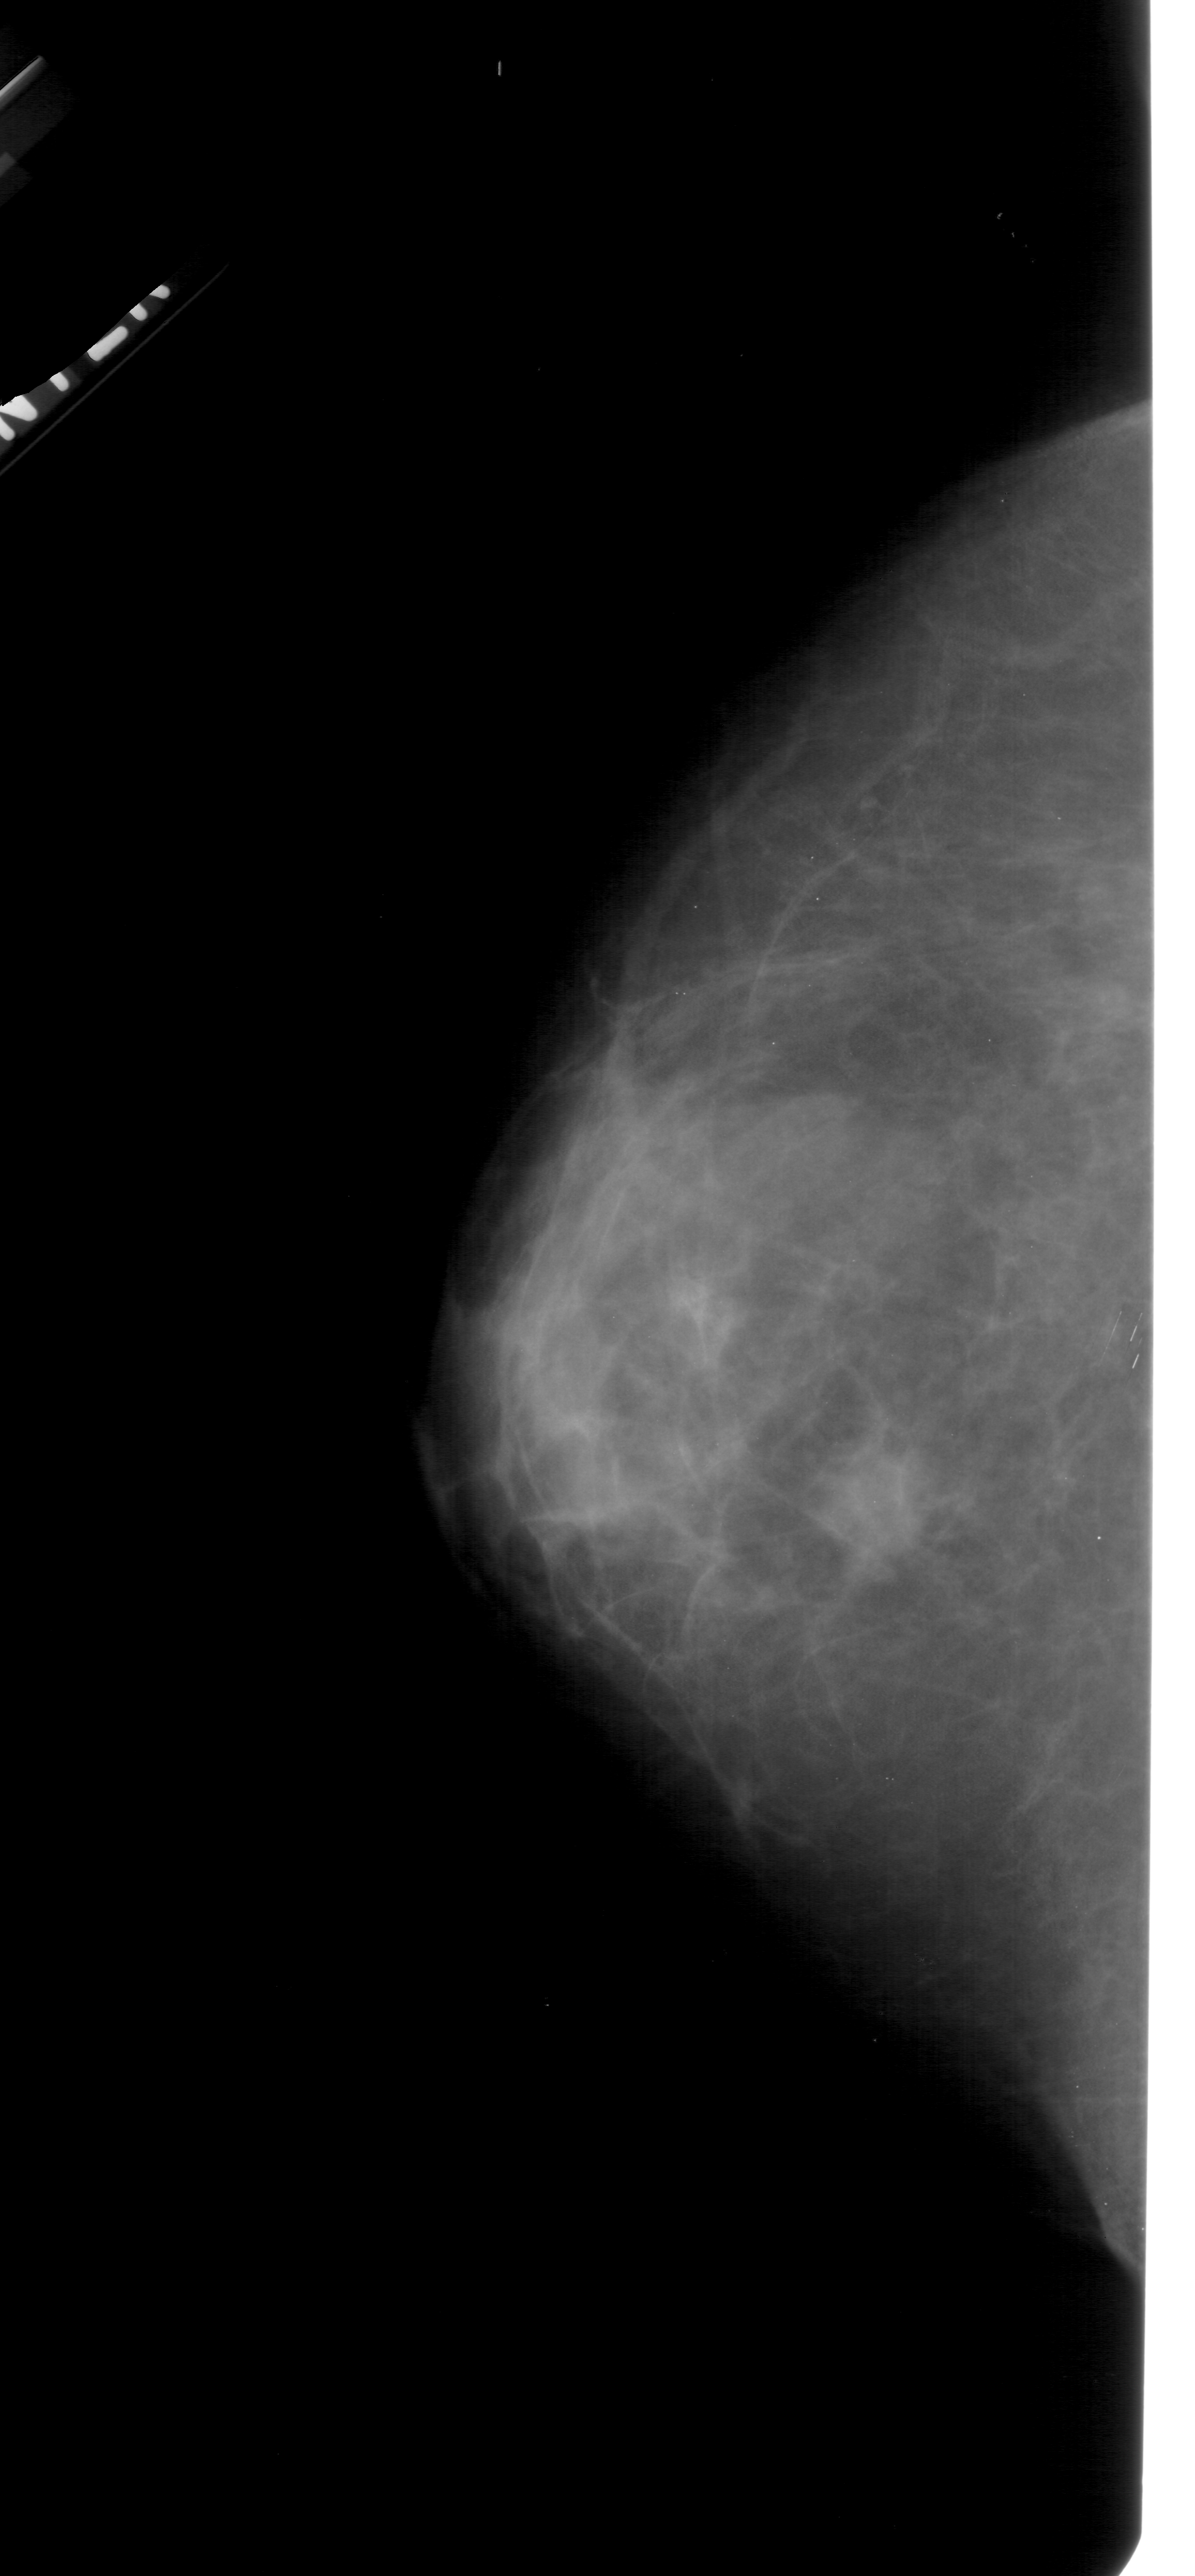
Digitized screen-film mammogram; left breast; CC view; BI-RADS breast density category 1 (scale 1–4).
- Finding: mass, shape irregular, margins ill defined; BI-RADS assessment category 4; pathology result (as recorded, not read from the image): malignant.